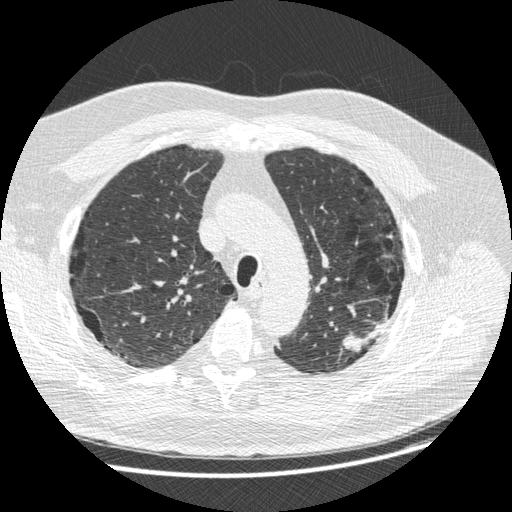
Low-dose screening chest CT, one axial slice; position 197 of 258 along the scan axis; 120 kVp; lung window (W 1500 / L -600 HU); 512 × 512 image matrix.
Structures marked on this image (manually delineated by an expert):
- lesion 1 (tumor, upper lobe of left lung): bounding box [x1, y1, x2, y2] px = [342, 322, 384, 352]